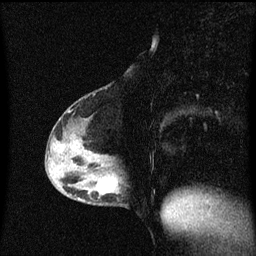
Breast MRI (dynamic contrast-enhanced), one sagittal slice. Position 27 of 60 along the scan axis. Dynamic contrast-enhanced series, image 2 of 3 at this slice position (ordered by acquisition). 1.5 T. TE 4.2 ms, TR 8.4 ms. 2 mm slice thickness. 256 × 256 image matrix. Patient: female, 40 years.
Outlined on this slice (semi-automatic segmentation, software-assisted and operator-edited):
- analysis volume of interest (the breast-tissue region the enhancement analysis was run in; not a lesion): bounding box [x1, y1, x2, y2] px = [82, 172, 124, 207]
- tumour enhancement mask (voxels above the 70 % enhancement threshold inside the analysis volume of interest): [116, 182, 118, 187]